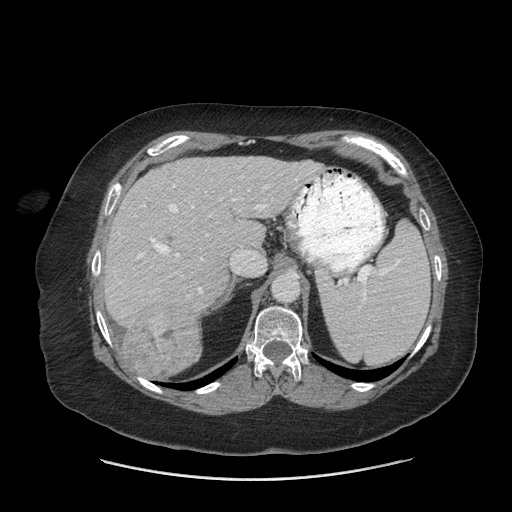
Contrast-enhanced abdominal CT (liver protocol), one axial slice; reconstruction kernel STANDARD; 140 kVp; soft-tissue window (W 400 / L 40 HU); 2.5 mm slice thickness; 512 × 512 image matrix, field of view 420 × 420 mm. From the clinical record (not read from this slice): diagnosis: hepatocellular carcinoma (patient treated with transarterial chemoembolisation; whether this scan precedes or follows treatment is not stated here); TNM stage (as recorded): Stage-IIIB.
Annotated regions visible in this slice (semi-automatic segmentation, software-assisted and operator-edited):
- liver parenchyma outside the tumour (the mass and vessels are separate outlines, so this box may not span the whole liver): bounding box (x1, y1, x2, y2) in pixels: (103, 156, 322, 329)
- mass: (124, 300, 202, 379)
- liver vessels: (119, 170, 314, 294)